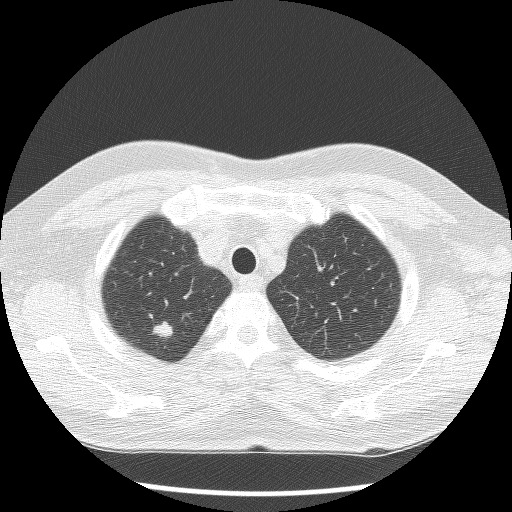
Axial slice from a low-dose chest CT screening exam, baseline screening round, lung window (W 1500 / L -600 HU), 2.5 mm slice thickness, slice 19 of 120 in the series, 512 × 512 image matrix. Male, age 70 years at enrolment.
Lesion marked by an expert reader, bounding box (x1, y1, x2, y2) in pixels: (134, 313, 186, 355). The exam's reader record, not a measurement of the box and not confirmed to be the same lesion: non-calcified nodule or mass ≥4 mm, right upper lobe, 12 × 10 mm, smooth margins, soft tissue attenuation. Official screen result: positive, change unspecified: nodule(s) >= 4 mm or enlarging nodule(s), mass(es), or other non-specific abnormalities suspicious for lung cancer. Later outcome: lung cancer diagnosed 14 days after this screen — large cell neuroendocrine carcinoma, right upper lobe, poorly differentiated (G3), stage IA (AJCC 6th edition), 15 mm at pathology.